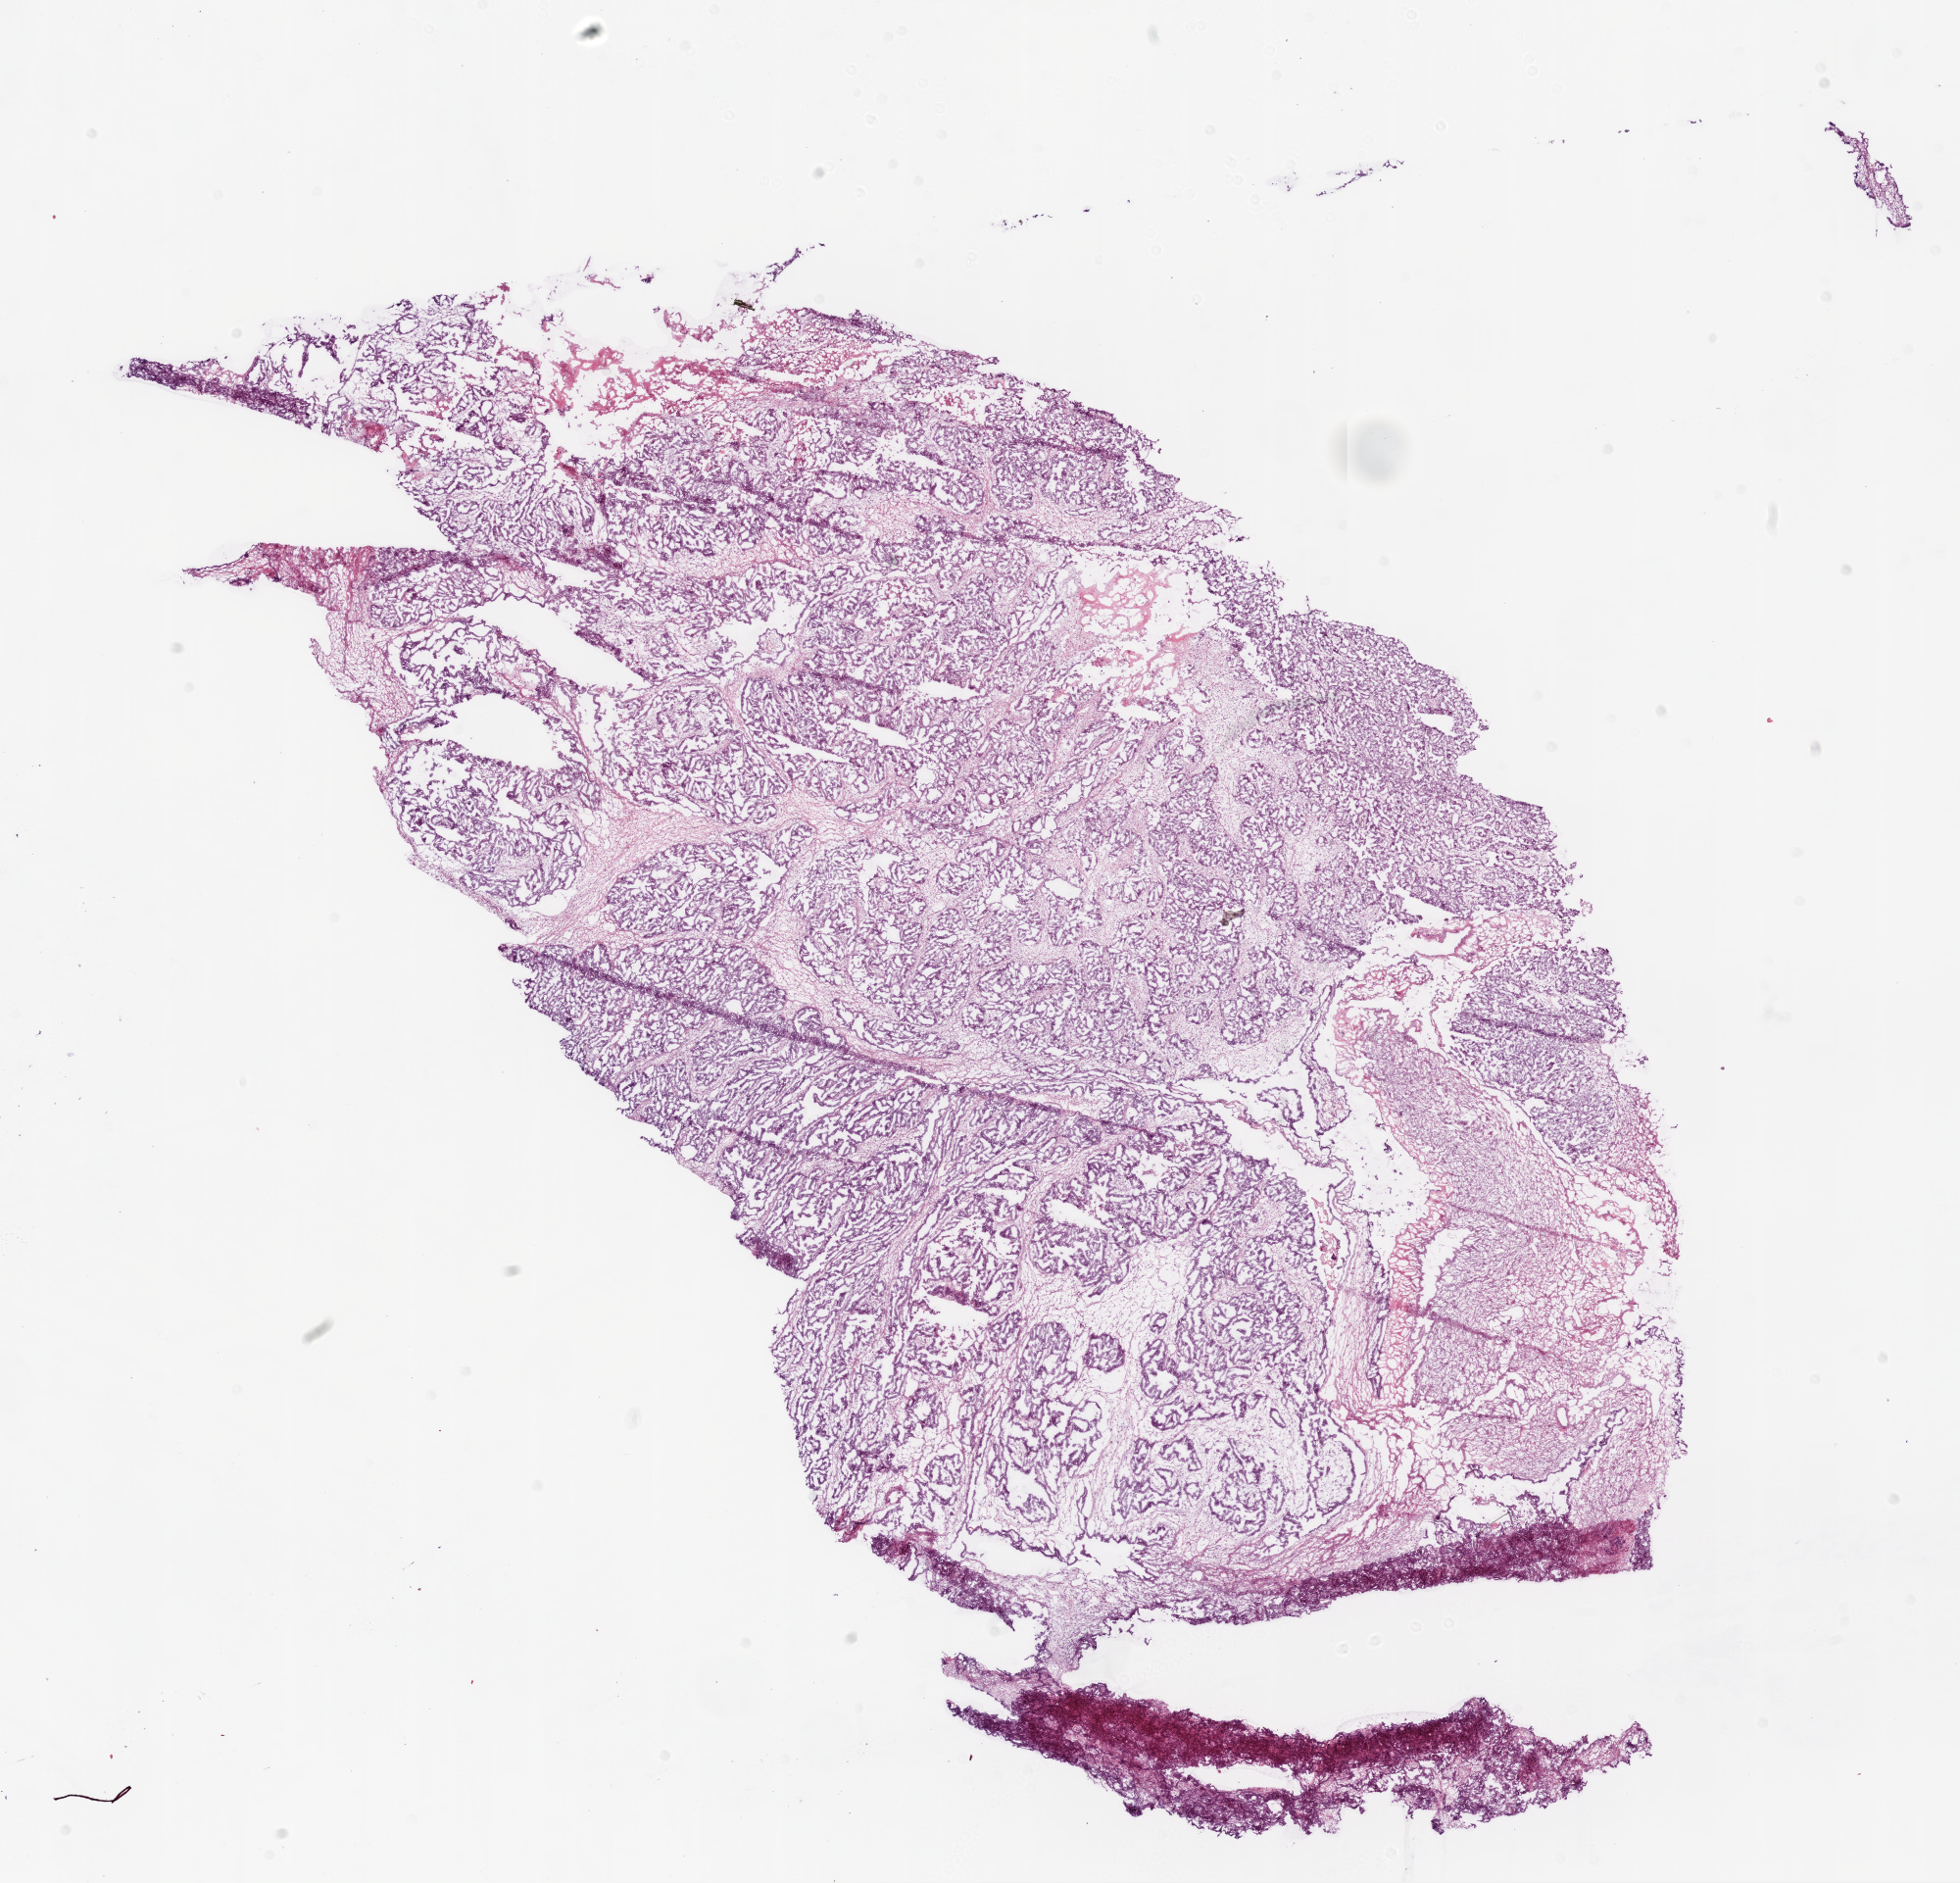
H&E-stained whole-slide image, low-resolution overview of the scanned area, about 16.0 x 15.4 mm (from a 20x scan), frozen section from the bottom of the tissue portion, sample: primary tumour, ovary. Female, age 51 years at initial diagnosis. Histologic grade: G3 (poorly differentiated). Slide review estimates, as recorded: tumour cells 90%, tumour nuclei 85%, normal cells 0%, stromal cells 7%, necrosis 3%. Infiltration values recorded for this section: lymphocyte infiltration 0%, monocyte infiltration 0%, neutrophil infiltration 0%.
FIGO stage: IV. Histologic diagnosis: Serous cystadenocarcinoma, NOS. Laterality: bilateral.